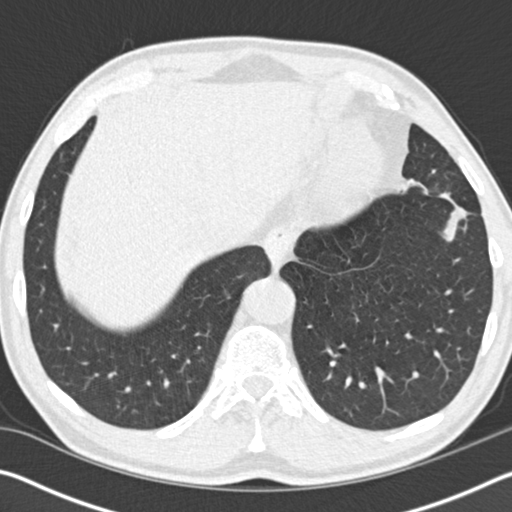
Low-dose screening chest CT, one axial slice; position 34 of 162 along the scan axis; lung window (W 1500 / L -600 HU); 2 mm slice thickness; 512 × 512 image matrix, field of view 340 × 340 mm.
Annotated regions visible in this slice (outlined manually by an expert reader):
- lesion 1 (tumor, upper lobe of left lung): bounding box [x1, y1, x2, y2] px = [443, 205, 467, 242]